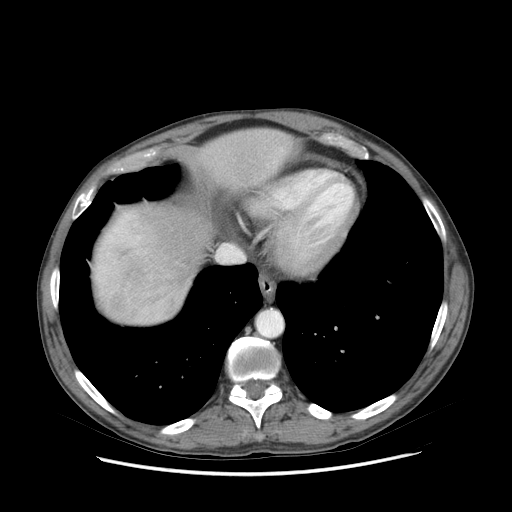
Contrast-enhanced abdominal CT (liver protocol), one axial slice; slice 72 of 89 in the series (ordered by position); soft-tissue window (W 400 / L 40 HU); 2.5 mm slice thickness; 512 × 512 image matrix, field of view 380 × 380 mm. From the clinical record (not read from this slice): diagnosis: hepatocellular carcinoma (patient treated with transarterial chemoembolisation; whether this scan precedes or follows treatment is not stated here); TNM stage (as recorded): Stage-IIIB; Child-Pugh class: A; tumour nodularity: multinodular.
Outlined on this slice (semi-automatic segmentation, software-assisted and operator-edited):
- abdominal aorta: box from (x=258, y=311) to (x=281, y=336) px
- liver parenchyma outside the tumour (the mass and vessels are separate outlines, so this box may not span the whole liver): (x=94, y=128)–(x=292, y=324)
- liver vessels: (x=98, y=214)–(x=141, y=282)